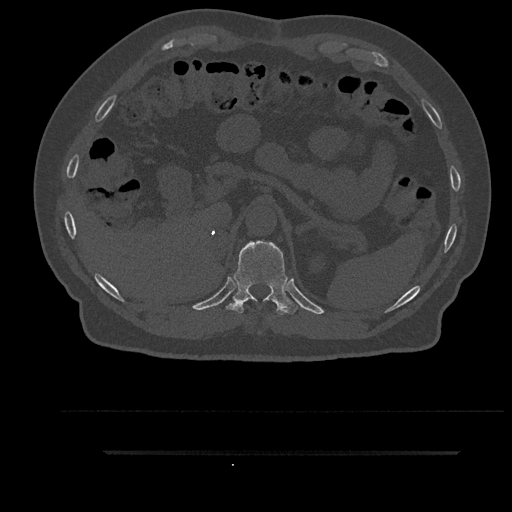
CT including the spine, one axial slice; slice 317 of 797 in the series (ordered by position); reconstruction kernel Br40s/3; 120 kVp; bone window (W 1800 / L 400 HU); 0.5 mm slice thickness; 512 × 512 image matrix, field of view 432 × 432 mm. Male patient, age 63 years. From the clinical record (not read from this slice): primary cancer: renal; vertebrae with lytic lesions (as recorded): T8.
Annotated regions visible in this slice (semi-automatic segmentation, software-assisted and operator-edited):
- T11 vertebra: bounding box [x1, y1, x2, y2] px = [226, 241, 297, 315]